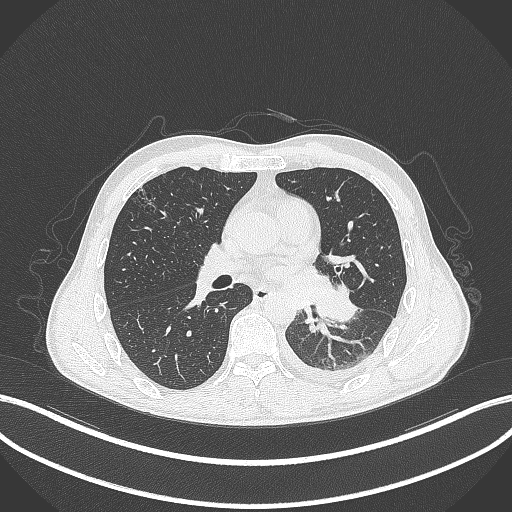
Chest CT, one axial slice; position 166 of 295 along the scan axis; 120 kVp; lung window (W 1500 / L -600 HU); 512 × 512 image matrix. Male patient, age 47 years. From the clinical record (not read from this slice): clinical TNM (as recorded): T3 N1 M1c; histopathological grade: G3.
Outlined on this slice (rectangle marked by the reading radiologist):
- lung tumour (recorded histology: small cell carcinoma): box from (x=317, y=280) to (x=362, y=325) px